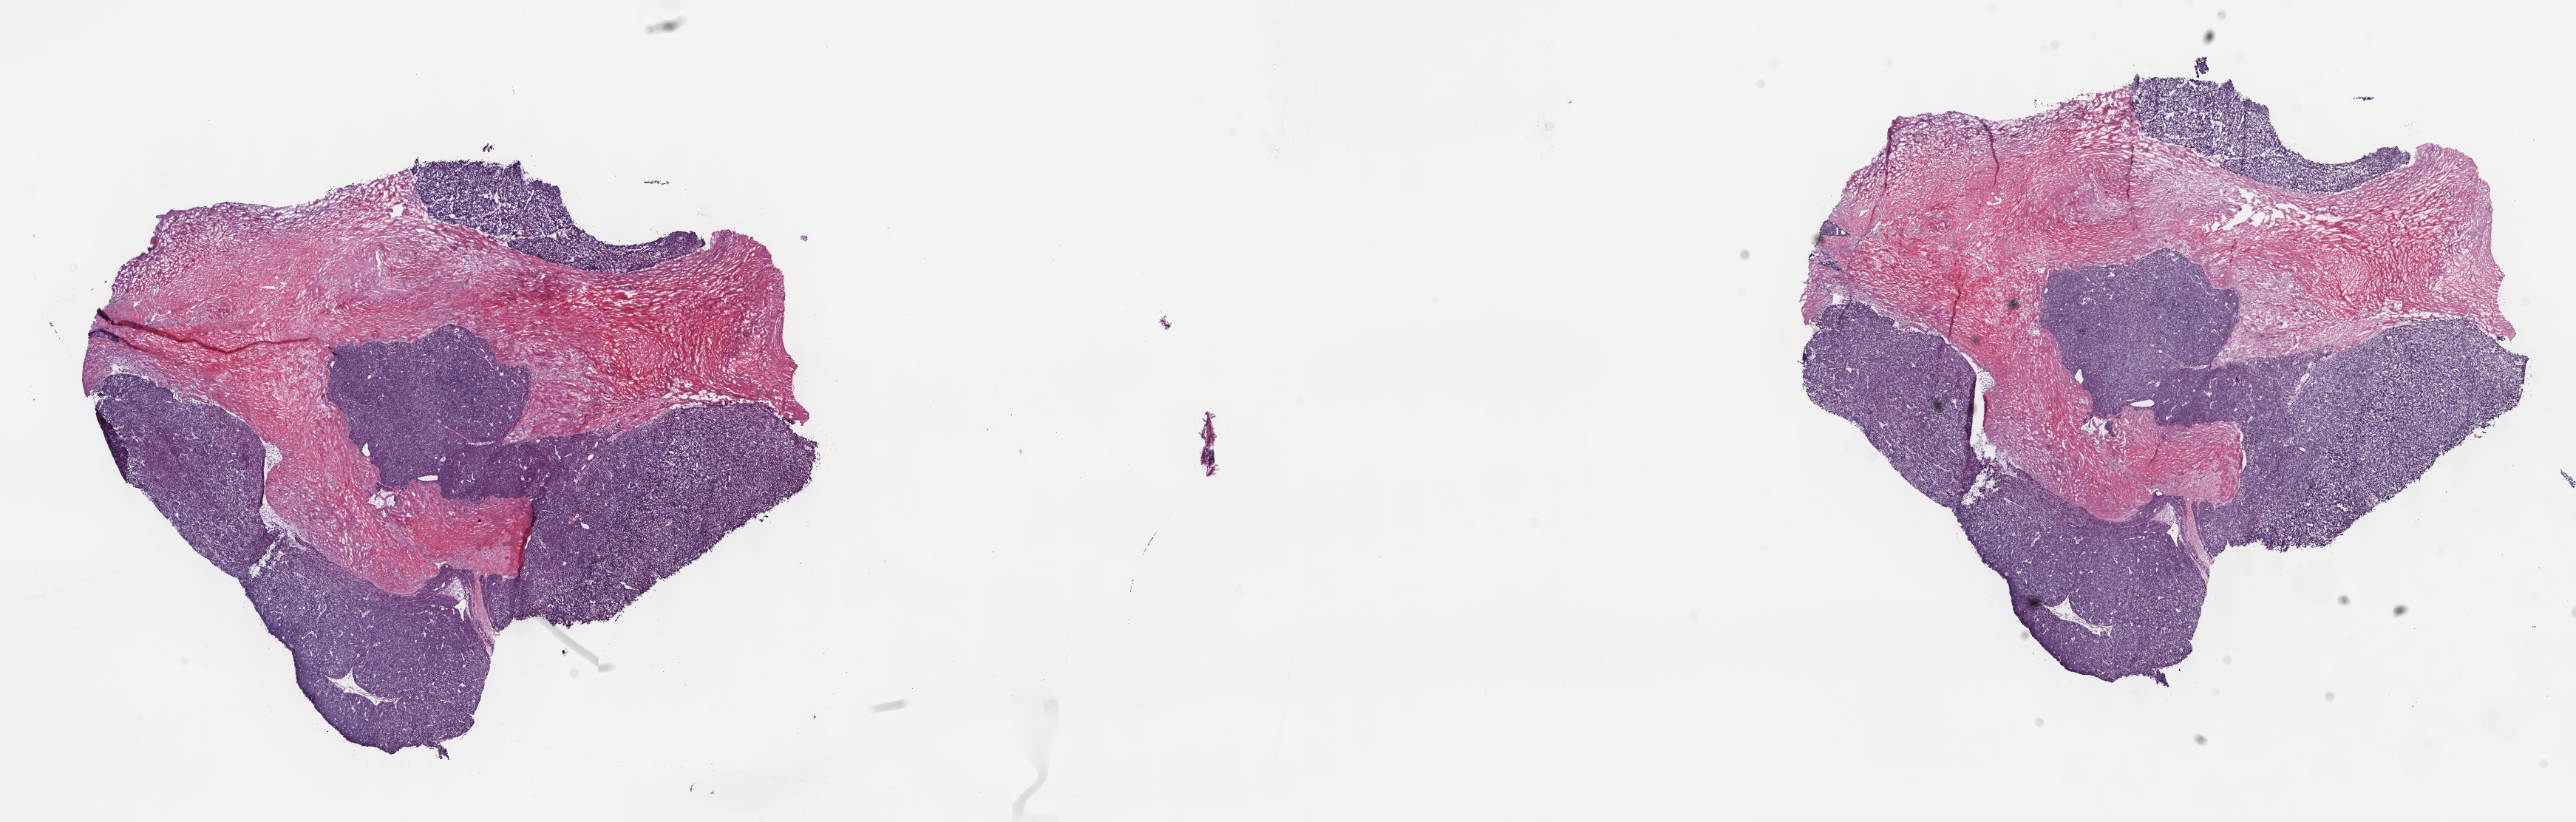
H&E whole-slide image, low-resolution overview of the scanned area, about 28.2 x 9.0 mm (acquisition: 40x scan). Frozen section from the top of the tissue portion. Thymus, primary tumour sample. Patient: female, age at initial diagnosis 70 years. Pathologist review of this section (percent, as recorded): tumour cells 50%, tumour nuclei 80%, normal cells 0%, stromal cells 50%, necrosis 0%. Infiltration values recorded for this section: lymphocyte infiltration 2%, monocyte infiltration 0%, neutrophil infiltration 0%.
Histologic diagnosis: Thymoma, type B3, malignant.